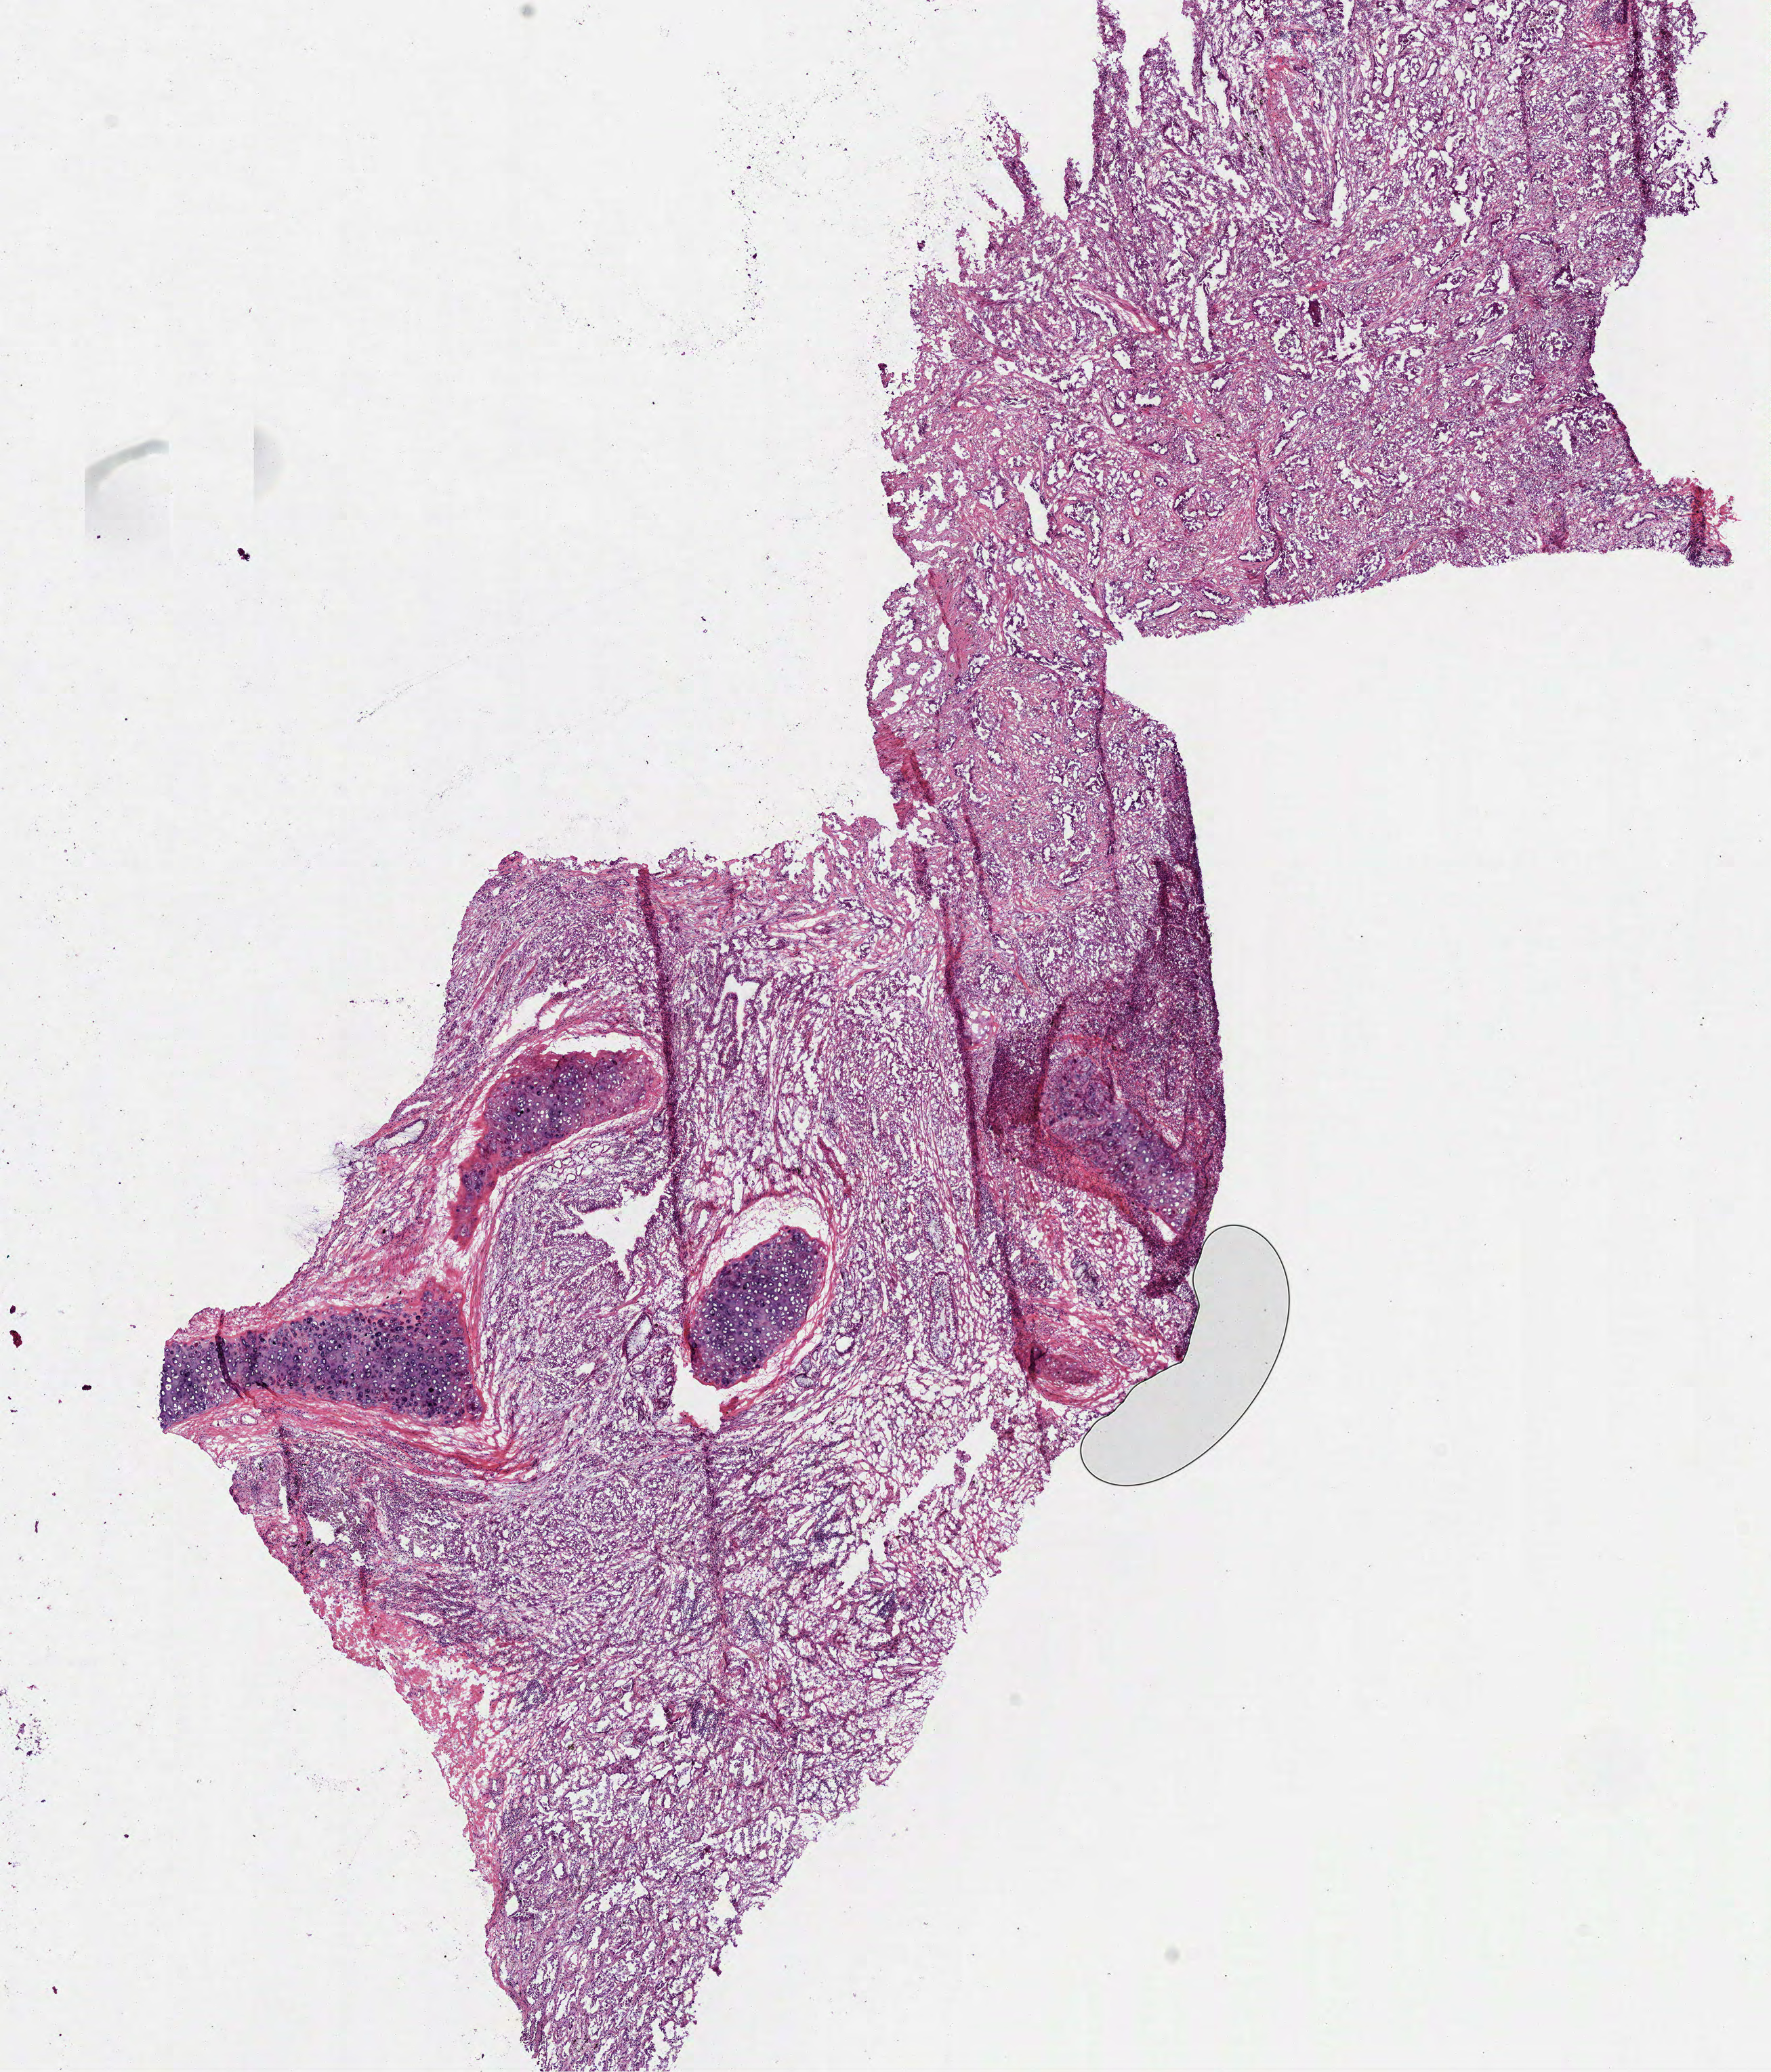
Whole-slide histology image, H&E-stained — a low-resolution overview of the entire scanned area, about 10.5 x 12.3 mm, frozen section, primary tumour sample from the lung. Female, age 49 years at initial diagnosis. Composition of this section per pathologist review: tumour cells 65%, tumour nuclei 75%.
Diagnosis: Adenocarcinoma with mixed subtypes (upper lobe, lung).